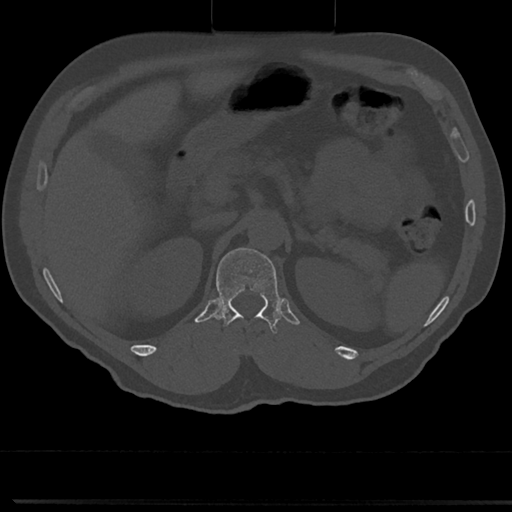
CT including the spine, one axial slice. Position 146 of 817 along the scan axis. Bone window (W 1800 / L 400 HU). 0.5 mm slice thickness. 512 × 512 image matrix. Male patient, age 61 years. From the clinical record (not read from this slice): primary cancer: prostate.
Structures marked on this image (semi-automatic segmentation, software-assisted and operator-edited):
- T12 vertebra: bounding box <212,246,280,340> (left, top, right, bottom; pixels)